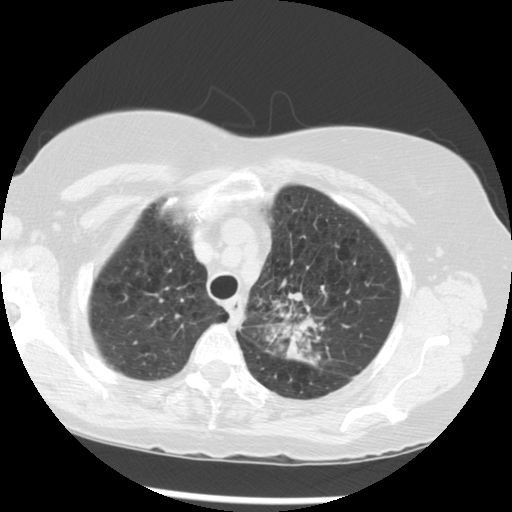
Low-dose screening chest CT, one axial slice. Slice 229 of 283 in the series (ordered by position). Lung window (W 1500 / L -600 HU). 2.5 mm slice thickness. 512 × 512 image matrix.
Structures marked on this image (outlined manually by an expert reader):
- lesion 1 (tumor, upper lobe of left lung): bounding box <283,292,322,363> (left, top, right, bottom; pixels)